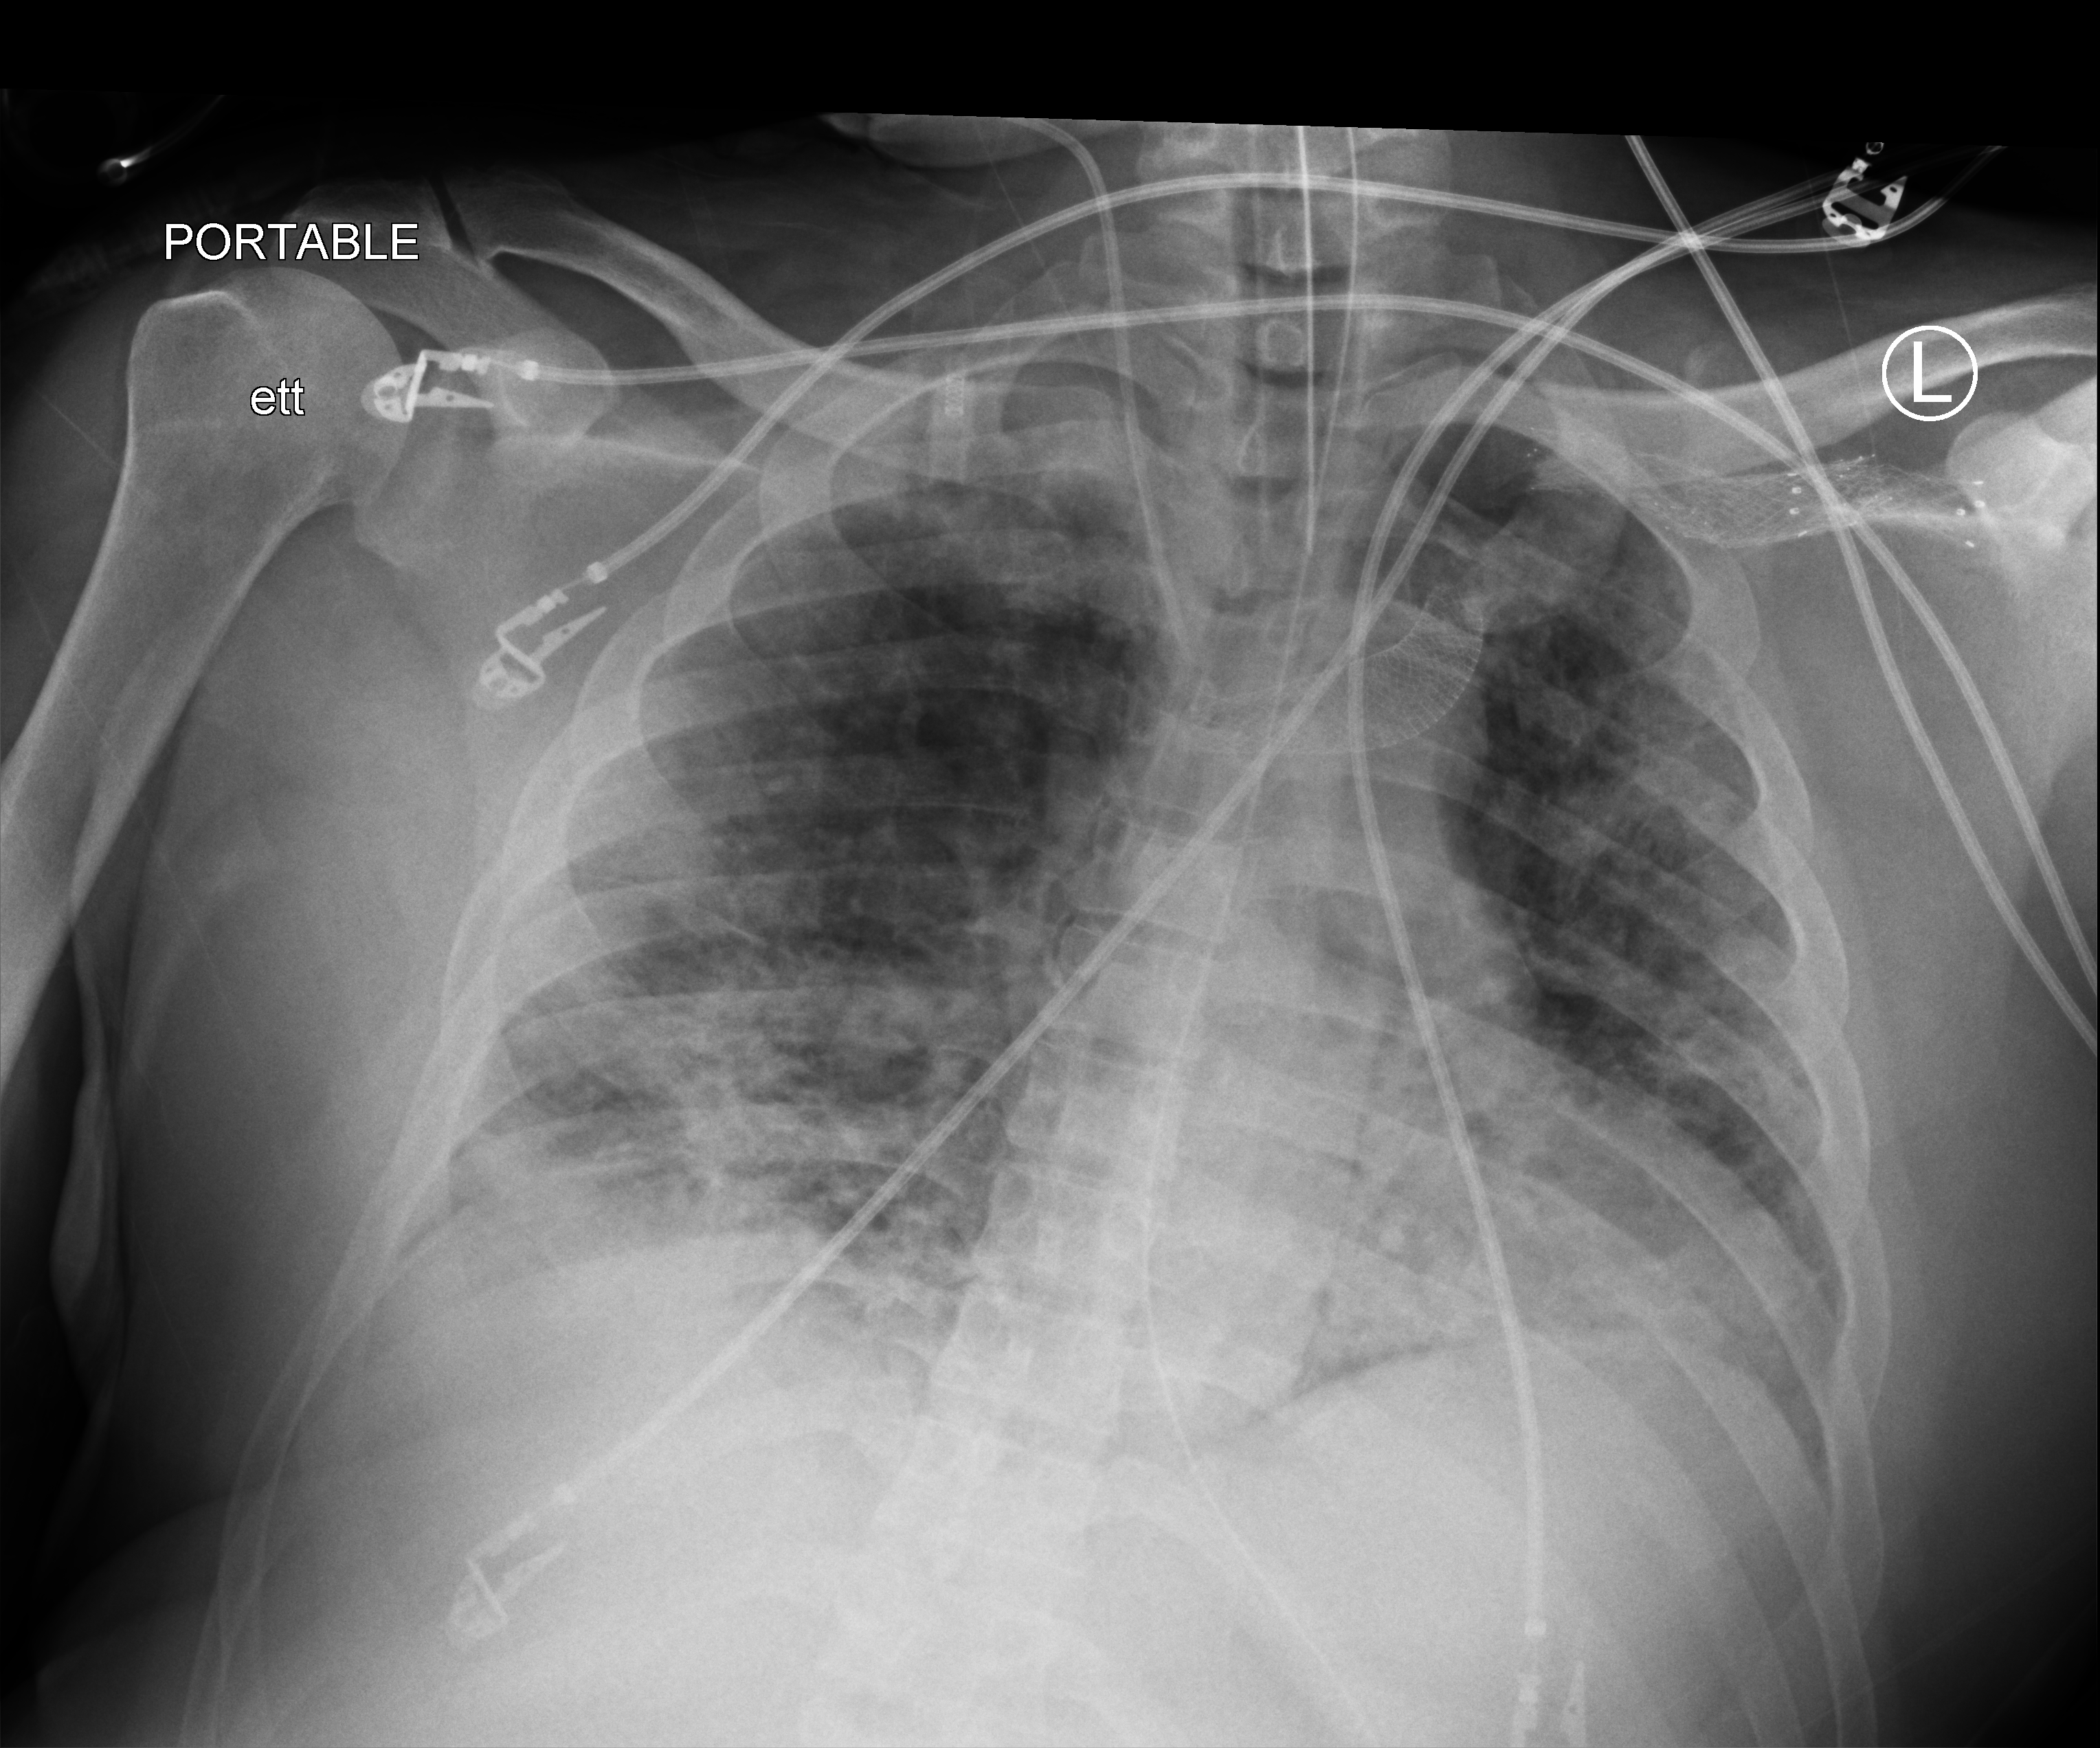
Bedside chest radiograph (computed radiography), anteroposterior (AP) projection. Patient hospitalised with COVID-19; male, aged 18–59 years.
Admission-level facts for this patient (not findings on this image; timing relative to this image not recorded):
- length of hospital stay: 41 days
- mechanically ventilated during this hospital stay: yes